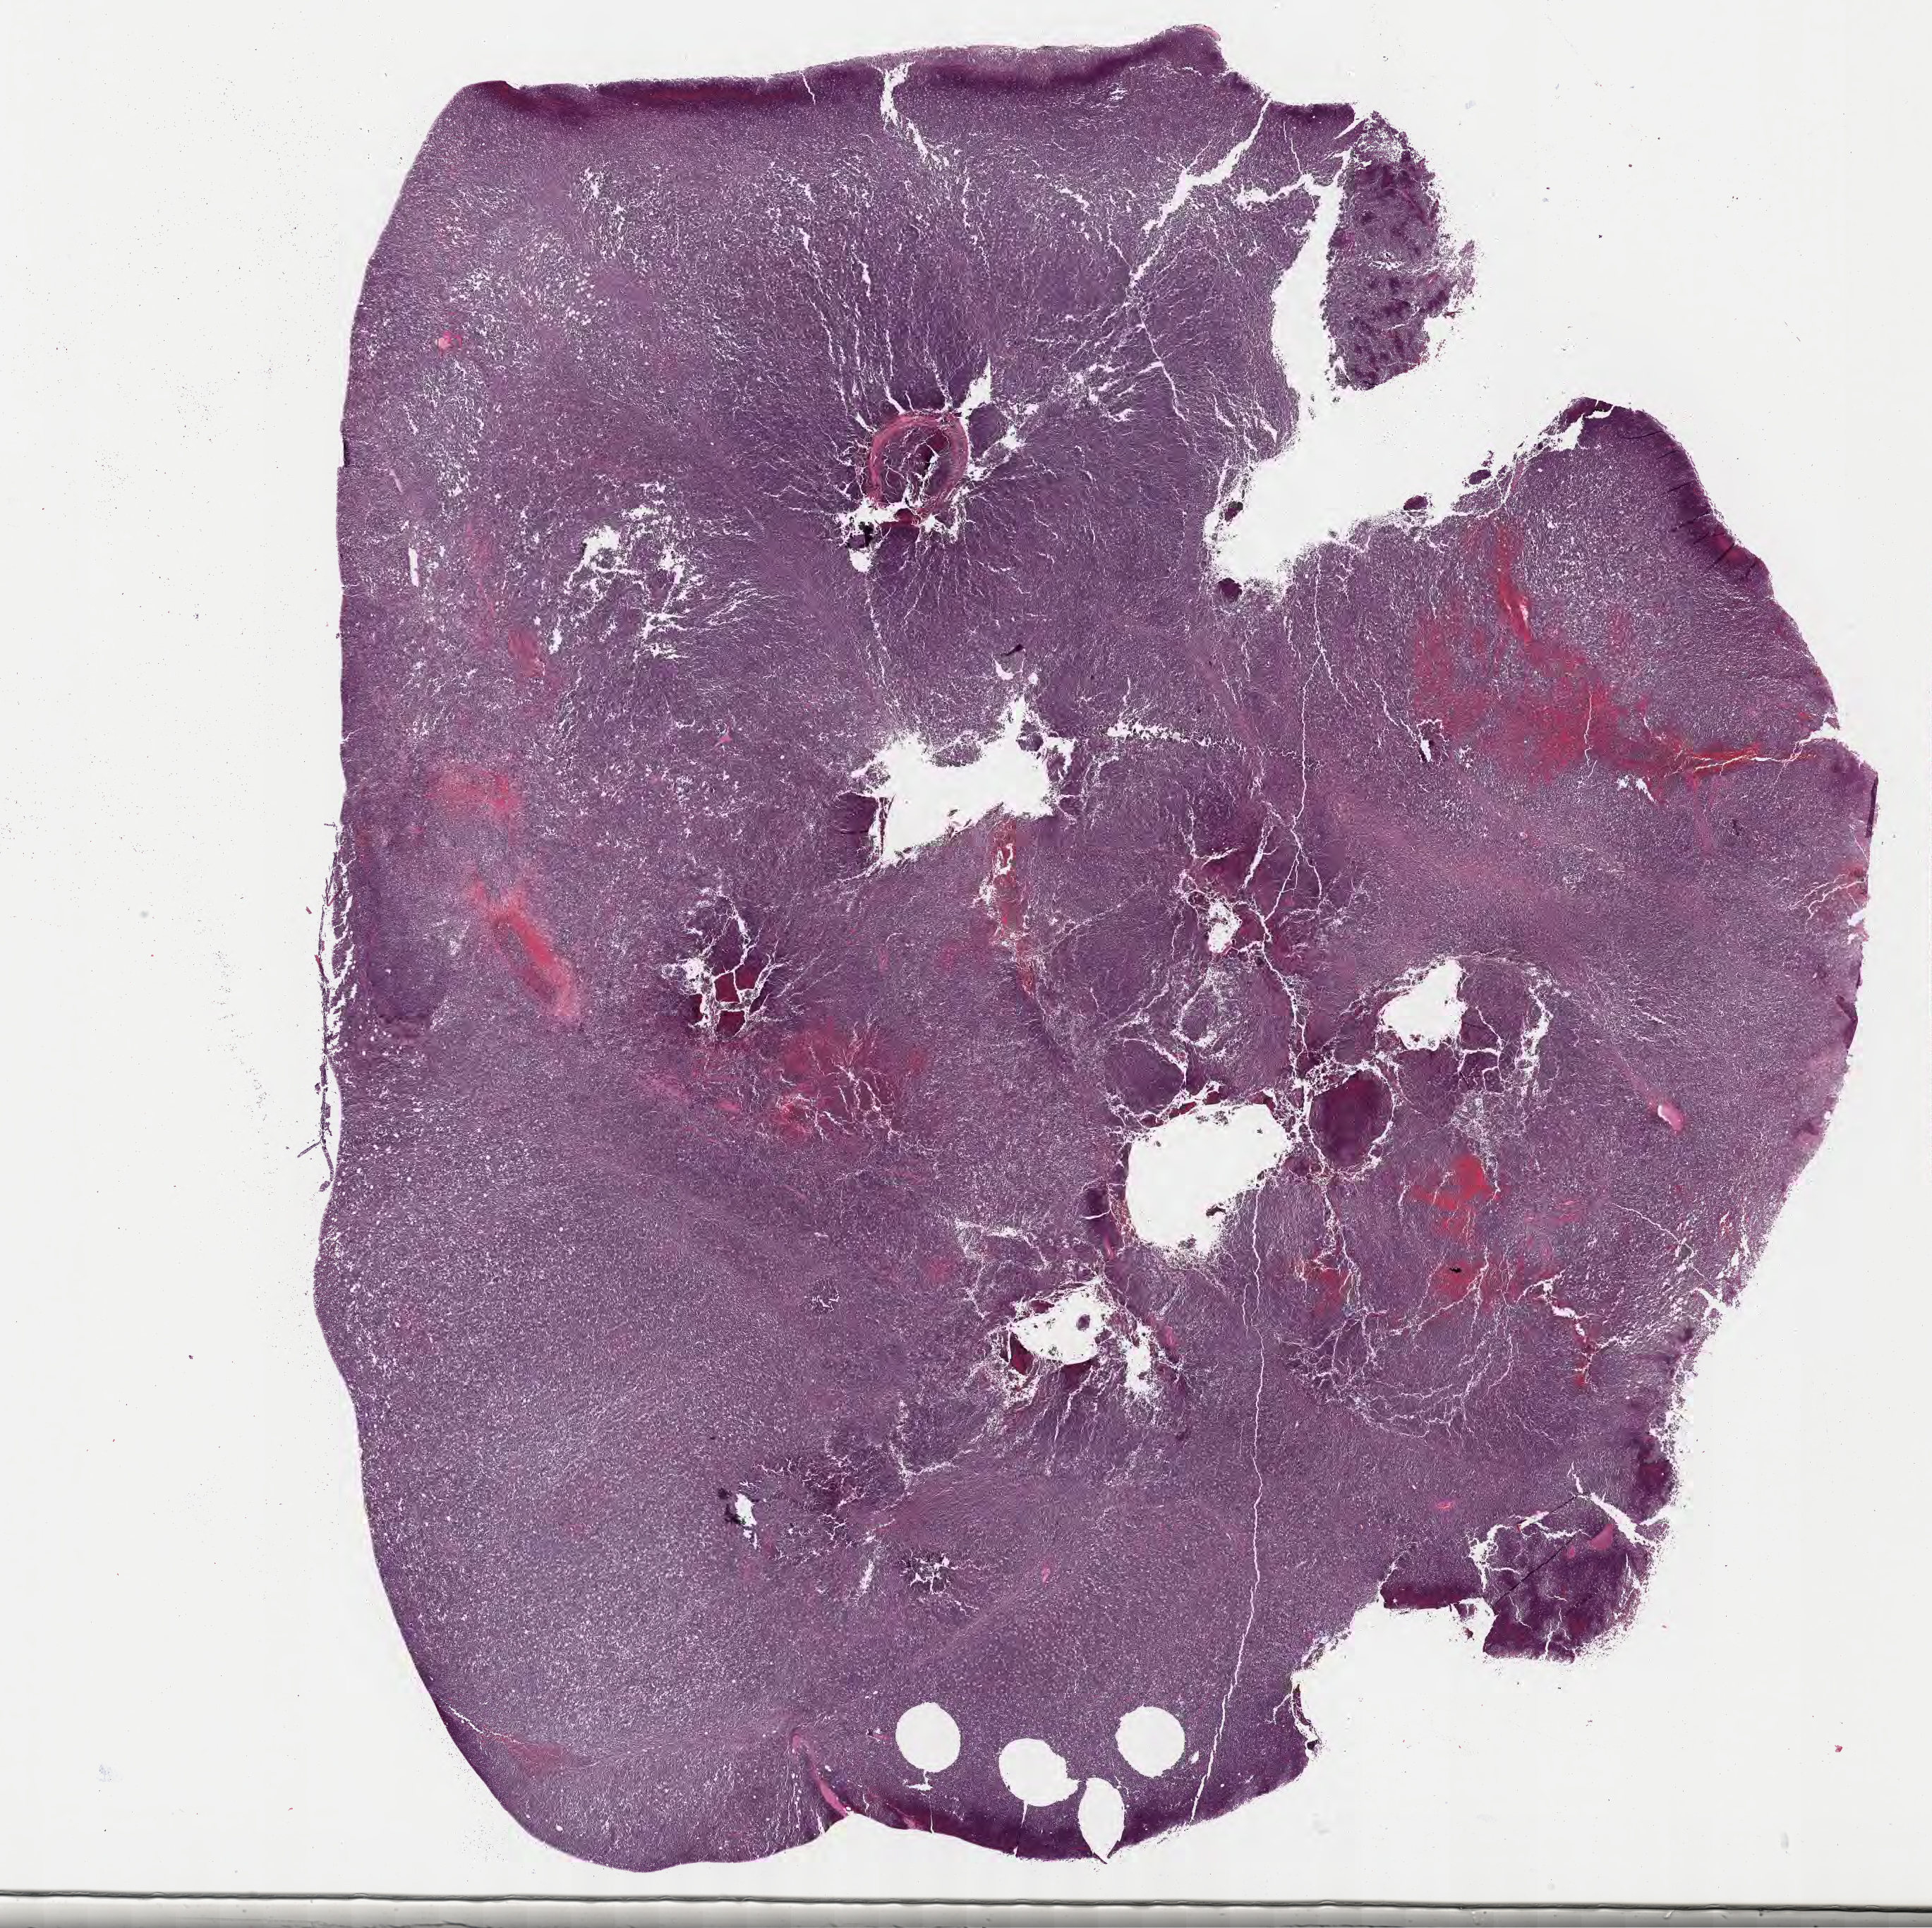
Haematoxylin and eosin whole-slide image — low-resolution overview of the scanned area, about 22.1 x 22.1 mm. Formalin-fixed, paraffin-embedded (FFPE) tissue. Primary tumor. Patient sex: male. Pathologist review of this section (percent, as recorded): tumor cells 95%, tumor nuclei 90%, stromal cells 5%, necrosis 0%, normal cells 0%. Inflammatory infiltration, as recorded: lymphocyte infiltration 50%, monocyte infiltration 30%, neutrophil infiltration 0%.
Section: top of the tissue portion. Diagnosis: Burkitt lymphoma, NOS. Ann Arbor stage (patient): Stage IV.